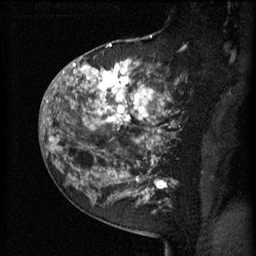
Breast MRI (dynamic contrast-enhanced), one sagittal slice. Slice 37 of 60 in the series (ordered by position). 3 images stored at this slice position (order not interpretable as contrast timing). 1.5 T. TE 4.2 ms, TR 11 ms. 256 × 256 image matrix. Patient: female, 52 years.
Outlined on this slice (semi-automatically segmented with operator editing):
- analysis volume of interest (the breast-tissue region the enhancement analysis was run in; not a lesion): bounding box <81,52,174,157> (left, top, right, bottom; pixels)
- tumour enhancement mask (voxels above the 70 % enhancement threshold inside the analysis volume of interest): <81,58,173,157>